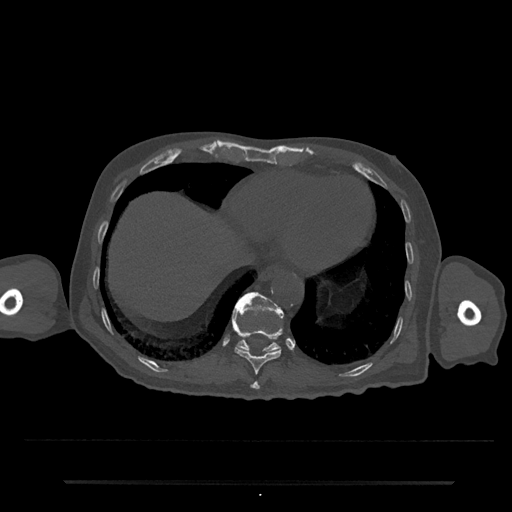
CT including the spine, one axial slice. Slice 295 of 797 in the series (ordered by position). 120 kVp. Bone window (W 1800 / L 400 HU). 512 × 512 image matrix, field of view 427 × 427 mm. Patient: male, 74 years. From the clinical record (not read from this slice): primary cancer: prostate.
Structures marked on this image (semi-automatic segmentation, software-assisted and operator-edited):
- T10 vertebra: bounding box (x1, y1, x2, y2) in pixels: (232, 315, 283, 374)
- T11 vertebra: (233, 292, 284, 353)
- T9 vertebra: (251, 381, 260, 390)